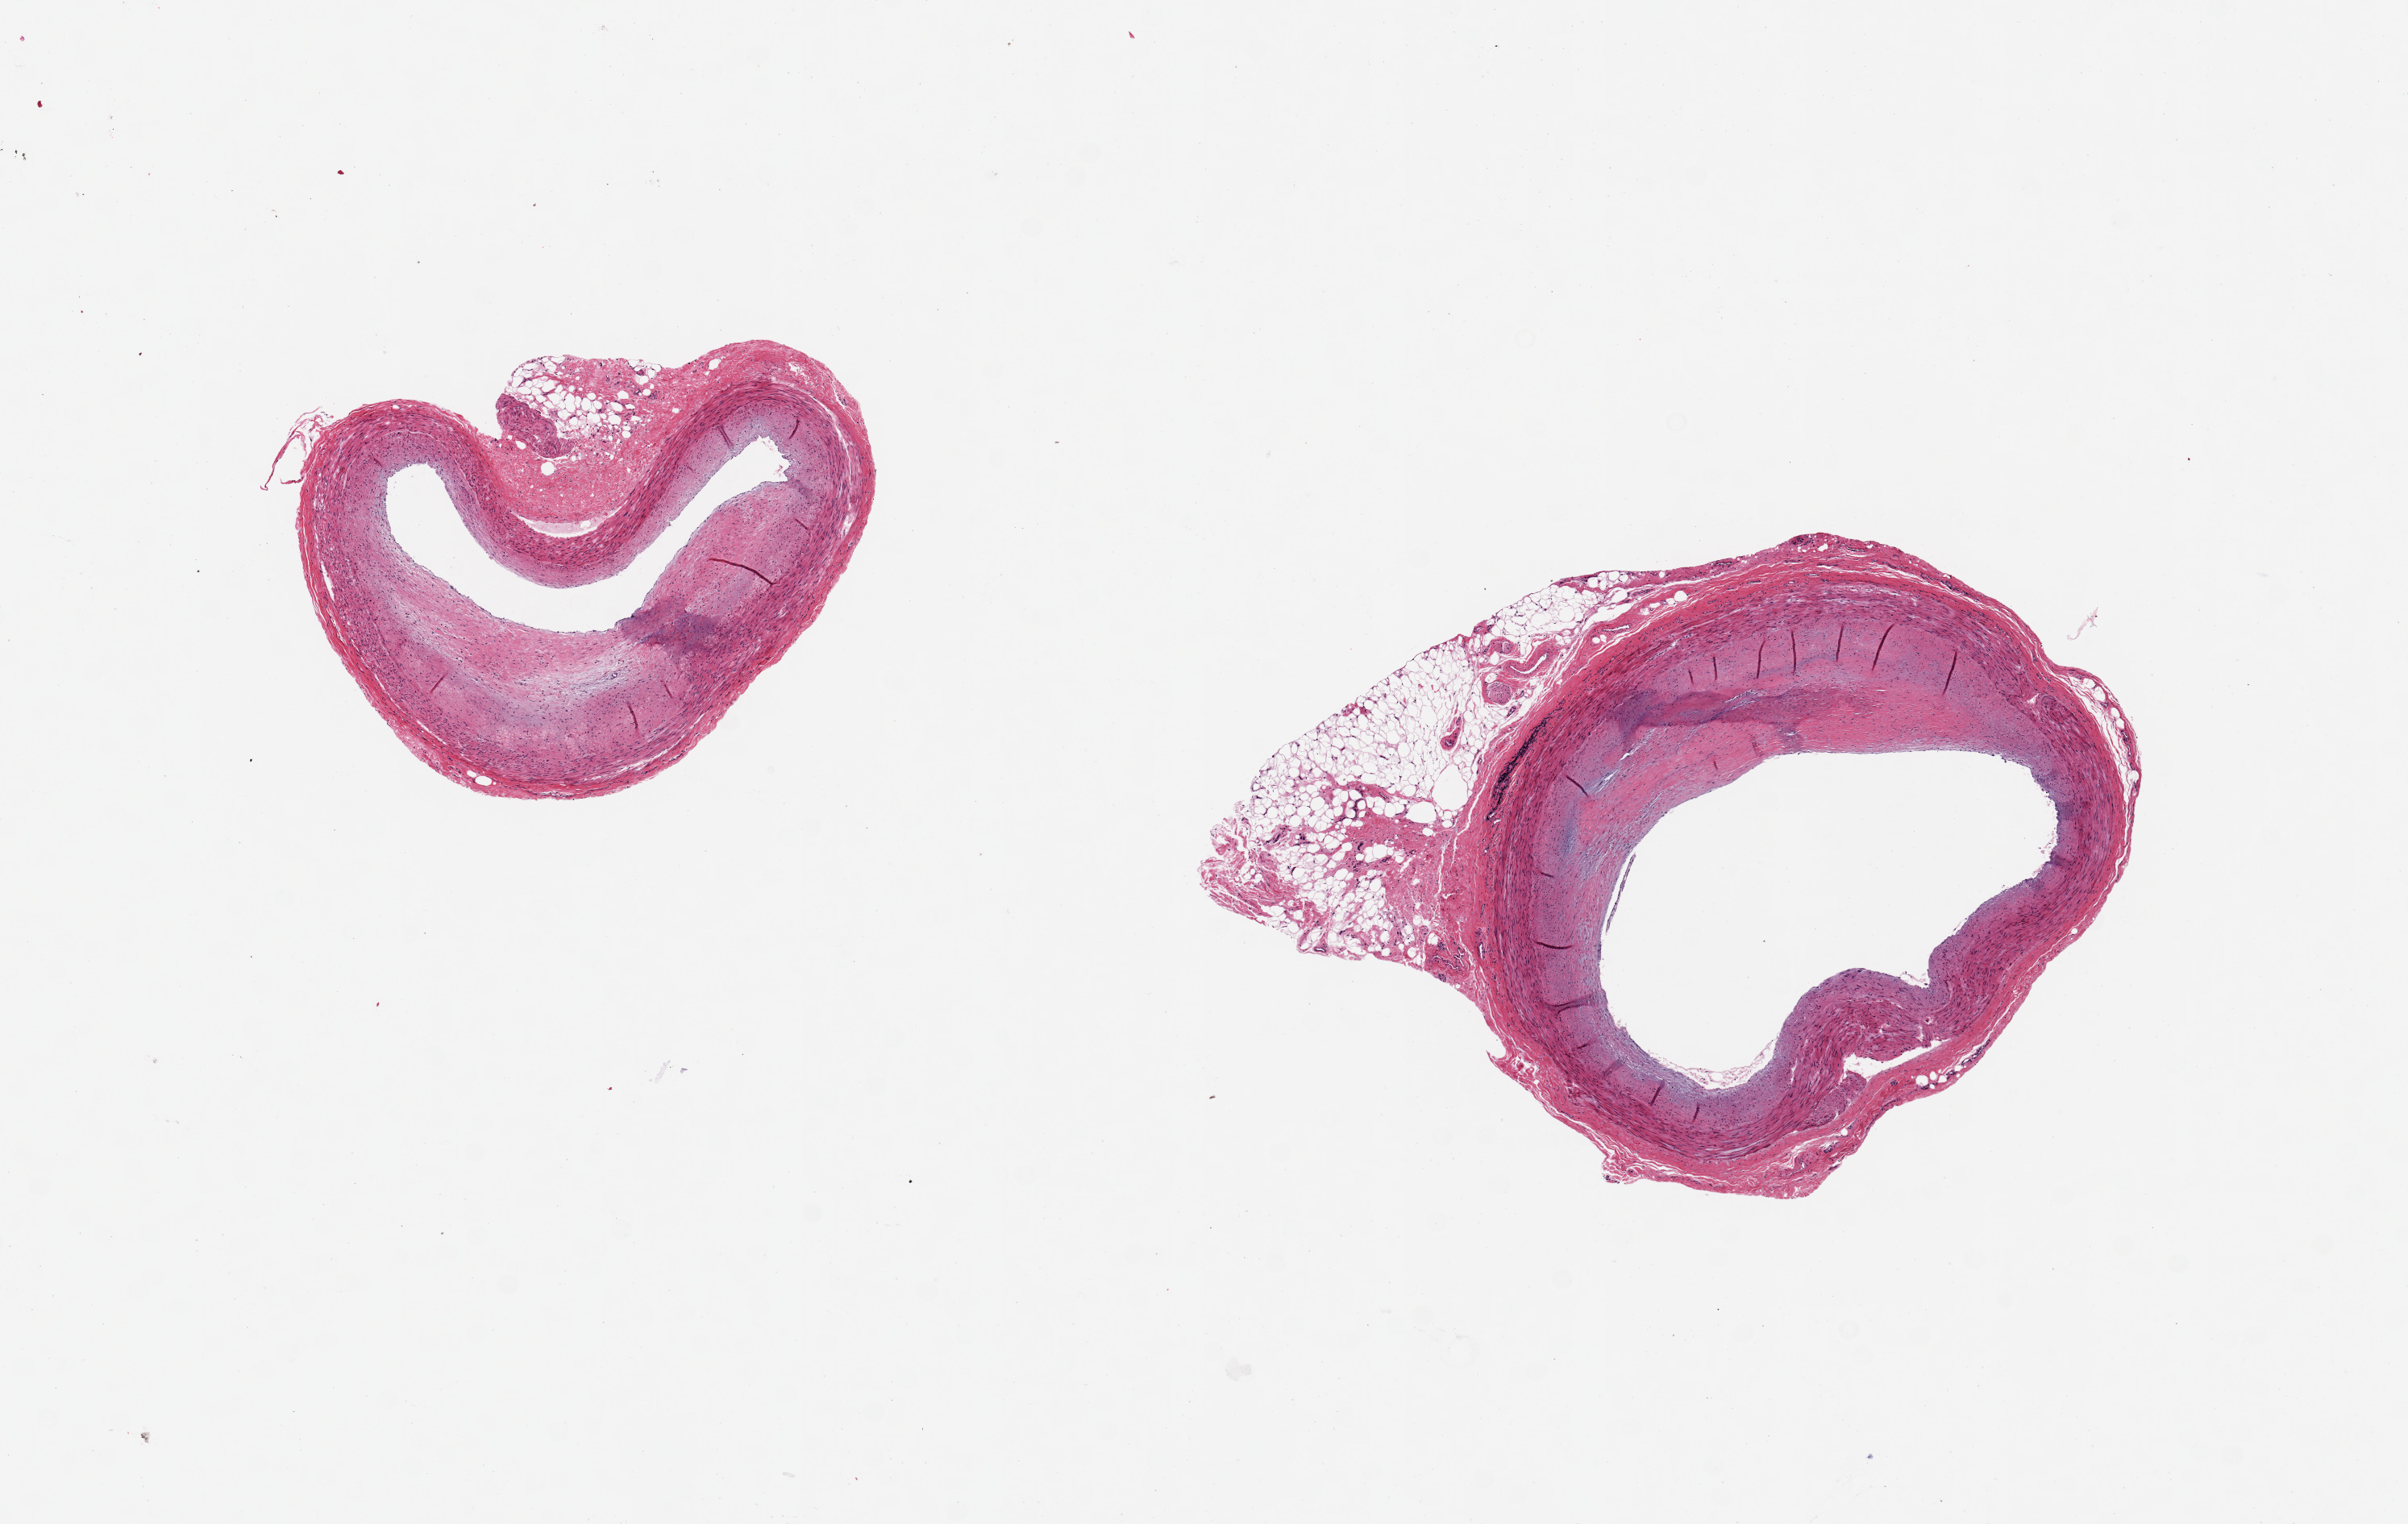
Hematoxylin and eosin (H&E) whole-slide image — whole scanned area (about 11.8 x 7.5 mm) shown as a low-resolution overview. PAXgene-fixed, paraffin-embedded tissue. Sampled site (target tissue): coronary artery. Tissue donor sample. Male donor.
Pathologist's review note for this sample: 2 pieces, 3x2 & 5x3mm; 50% atheromatous plaques; 10-20% peripheral fibroadipose.